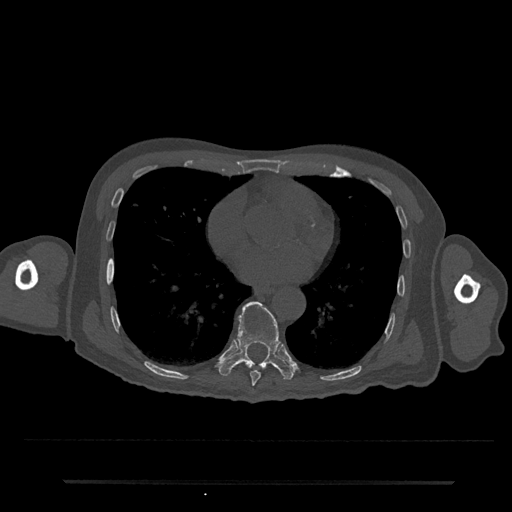
CT including the spine, one axial slice; slice 386 of 797 in the series (ordered by position); 120 kVp; bone window (W 1800 / L 400 HU); 0.5 mm slice thickness; 512 × 512 image matrix, field of view 427 × 427 mm. Male patient, age 74 years. From the clinical record (not read from this slice): primary cancer: prostate.
Annotated regions visible in this slice (semi-automatic segmentation, software-assisted and operator-edited):
- T8 vertebra: bounding box [x1, y1, x2, y2] px = [250, 370, 261, 386]
- T9 vertebra: [219, 301, 294, 380]